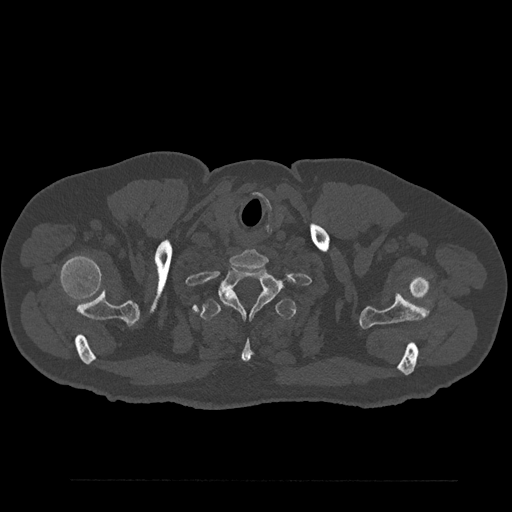
CT including the spine, one axial slice; position 746 of 797 along the scan axis; 120 kVp; bone window (W 1800 / L 400 HU); 0.5 mm slice thickness; 512 × 512 image matrix, field of view 430 × 430 mm. Patient: male, 61 years. From the clinical record (not read from this slice): primary cancer: prostate.
Annotated regions visible in this slice (semi-automatically segmented with operator editing):
- T1 vertebra: box from (x=218, y=268) to (x=291, y=318) px
- T2 vertebra: (x=200, y=297)–(x=296, y=362)